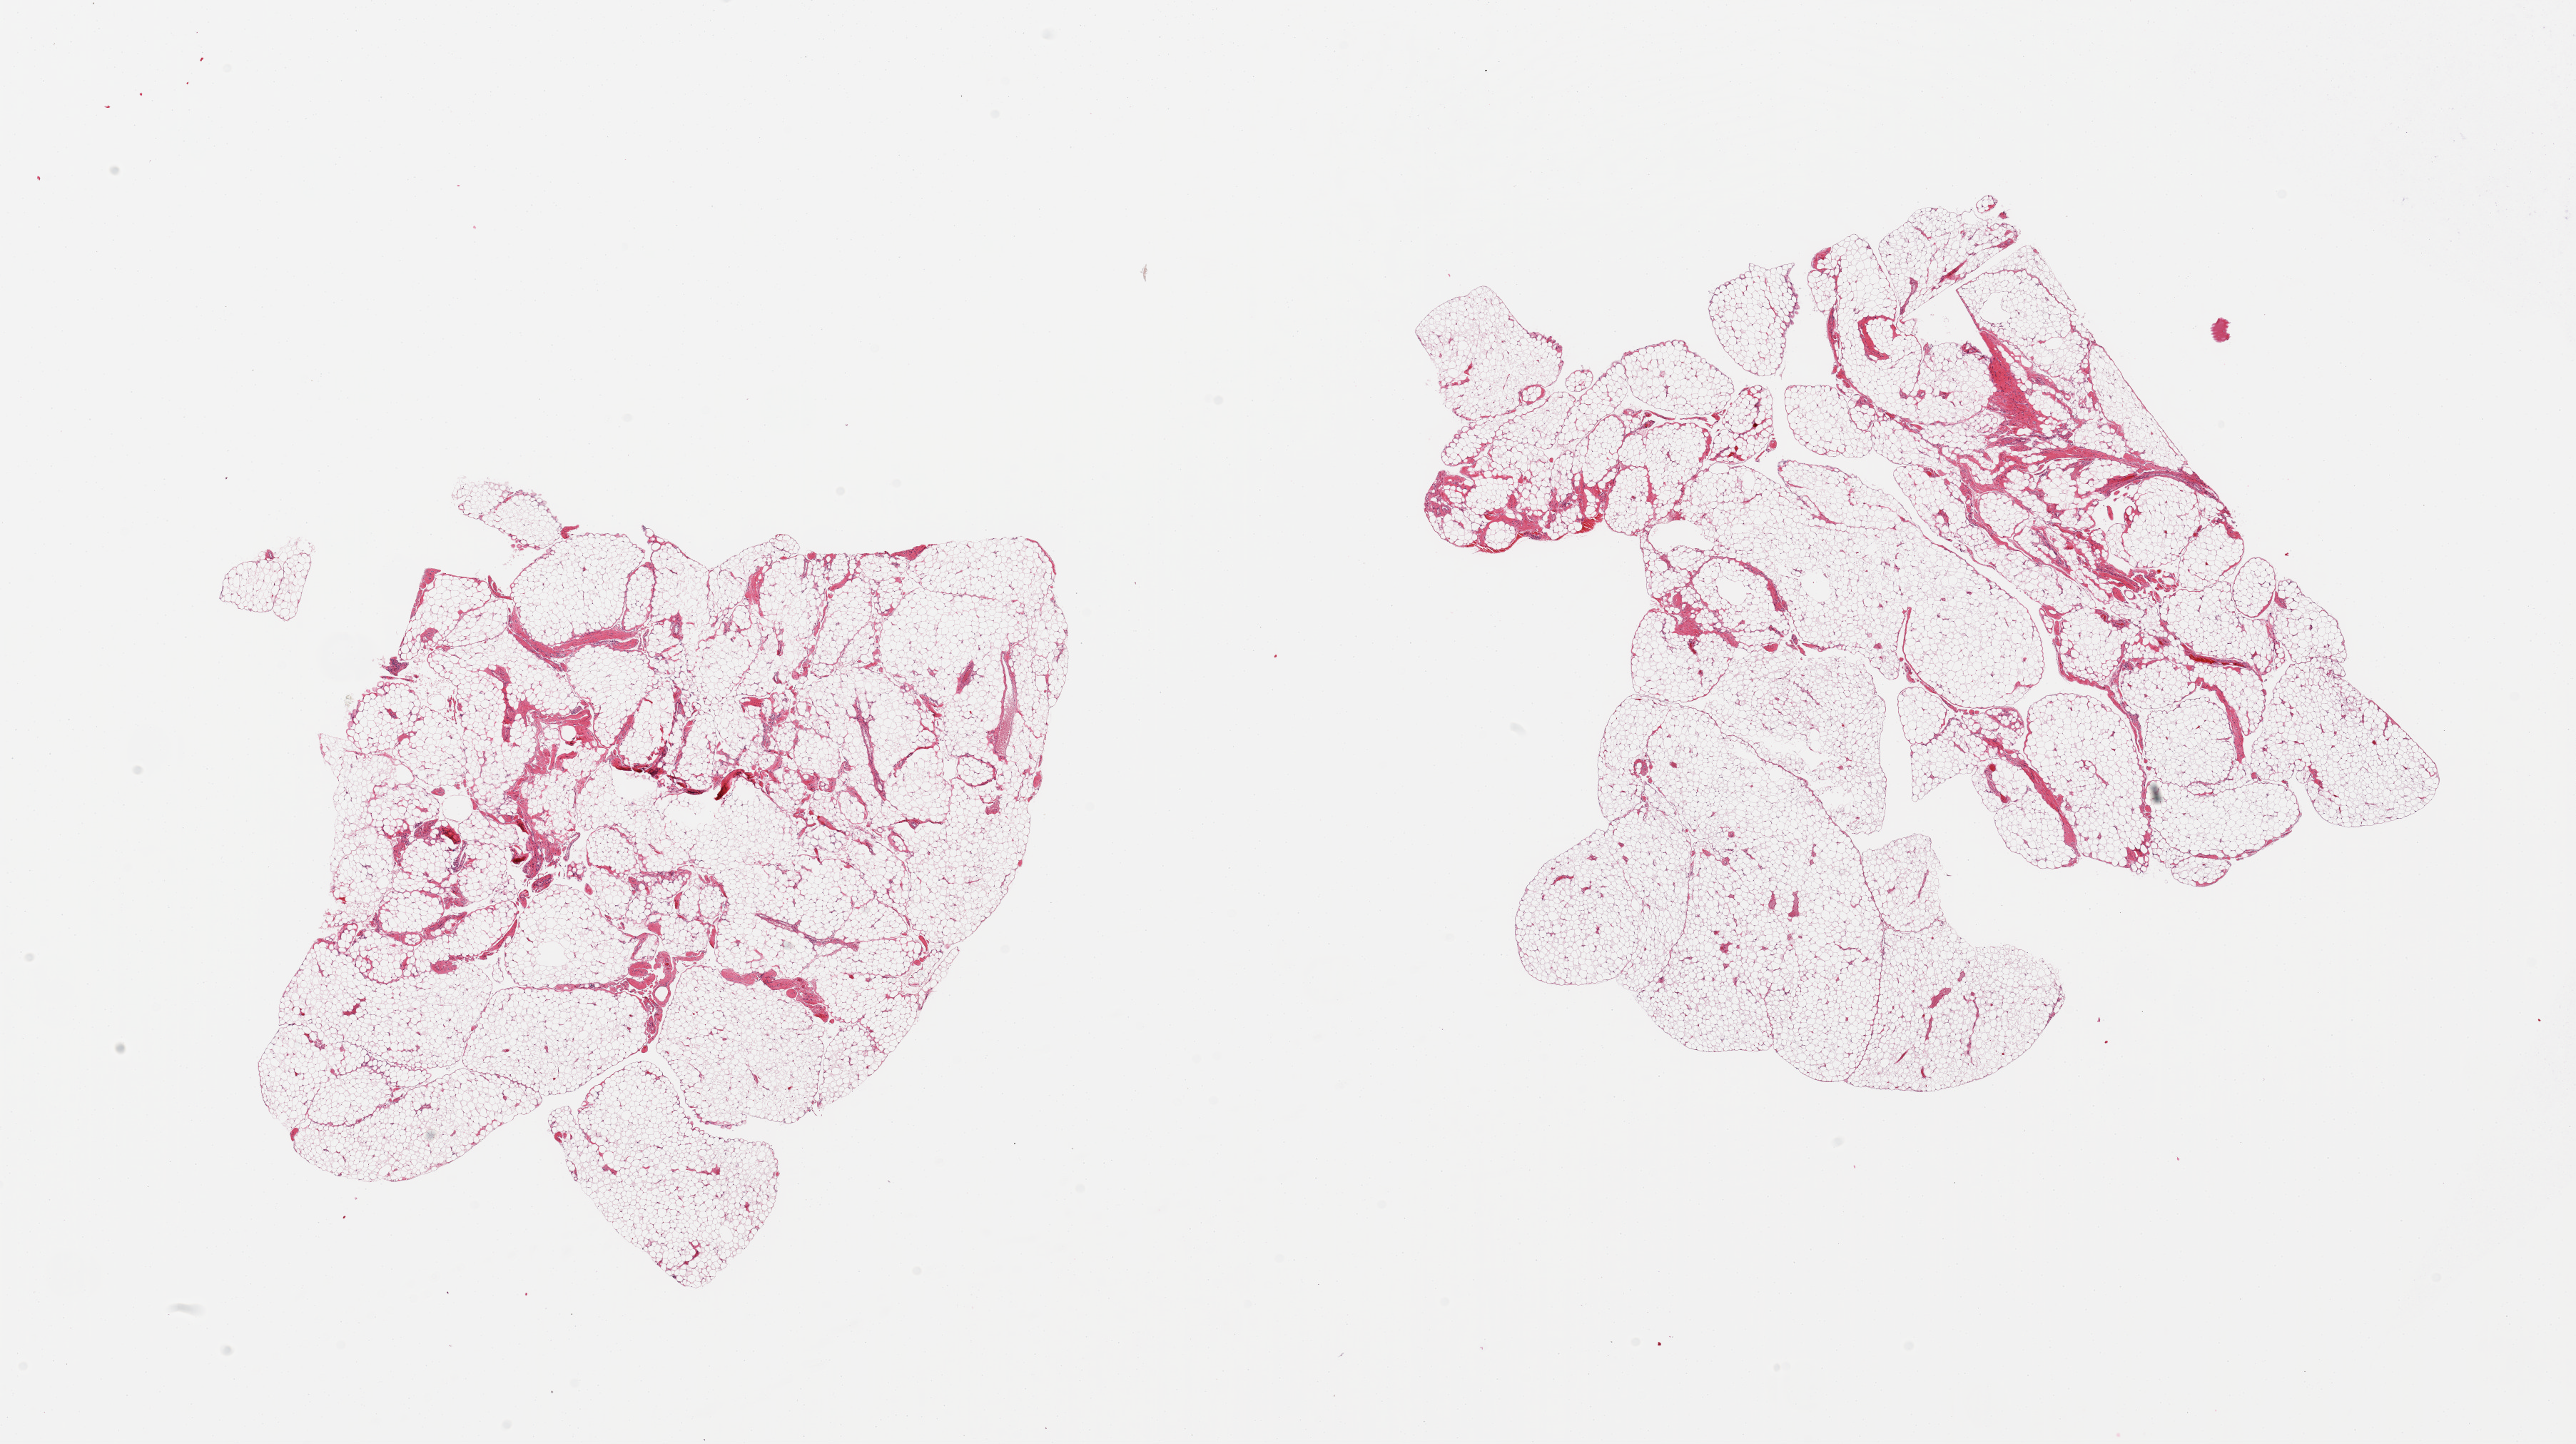
Digitized hematoxylin and eosin (H&E)-stained section, shown as a low-resolution overview of the whole scanned area (about 28.5 x 16.0 mm, slide scanned at 20x), PAXgene-fixed paraffin-embedded (PFPE) section, sampled site (target tissue): omentum, tissue donor sample.
Review note (as recorded): 2 pieces, !0-20% fibrovascular tissue.